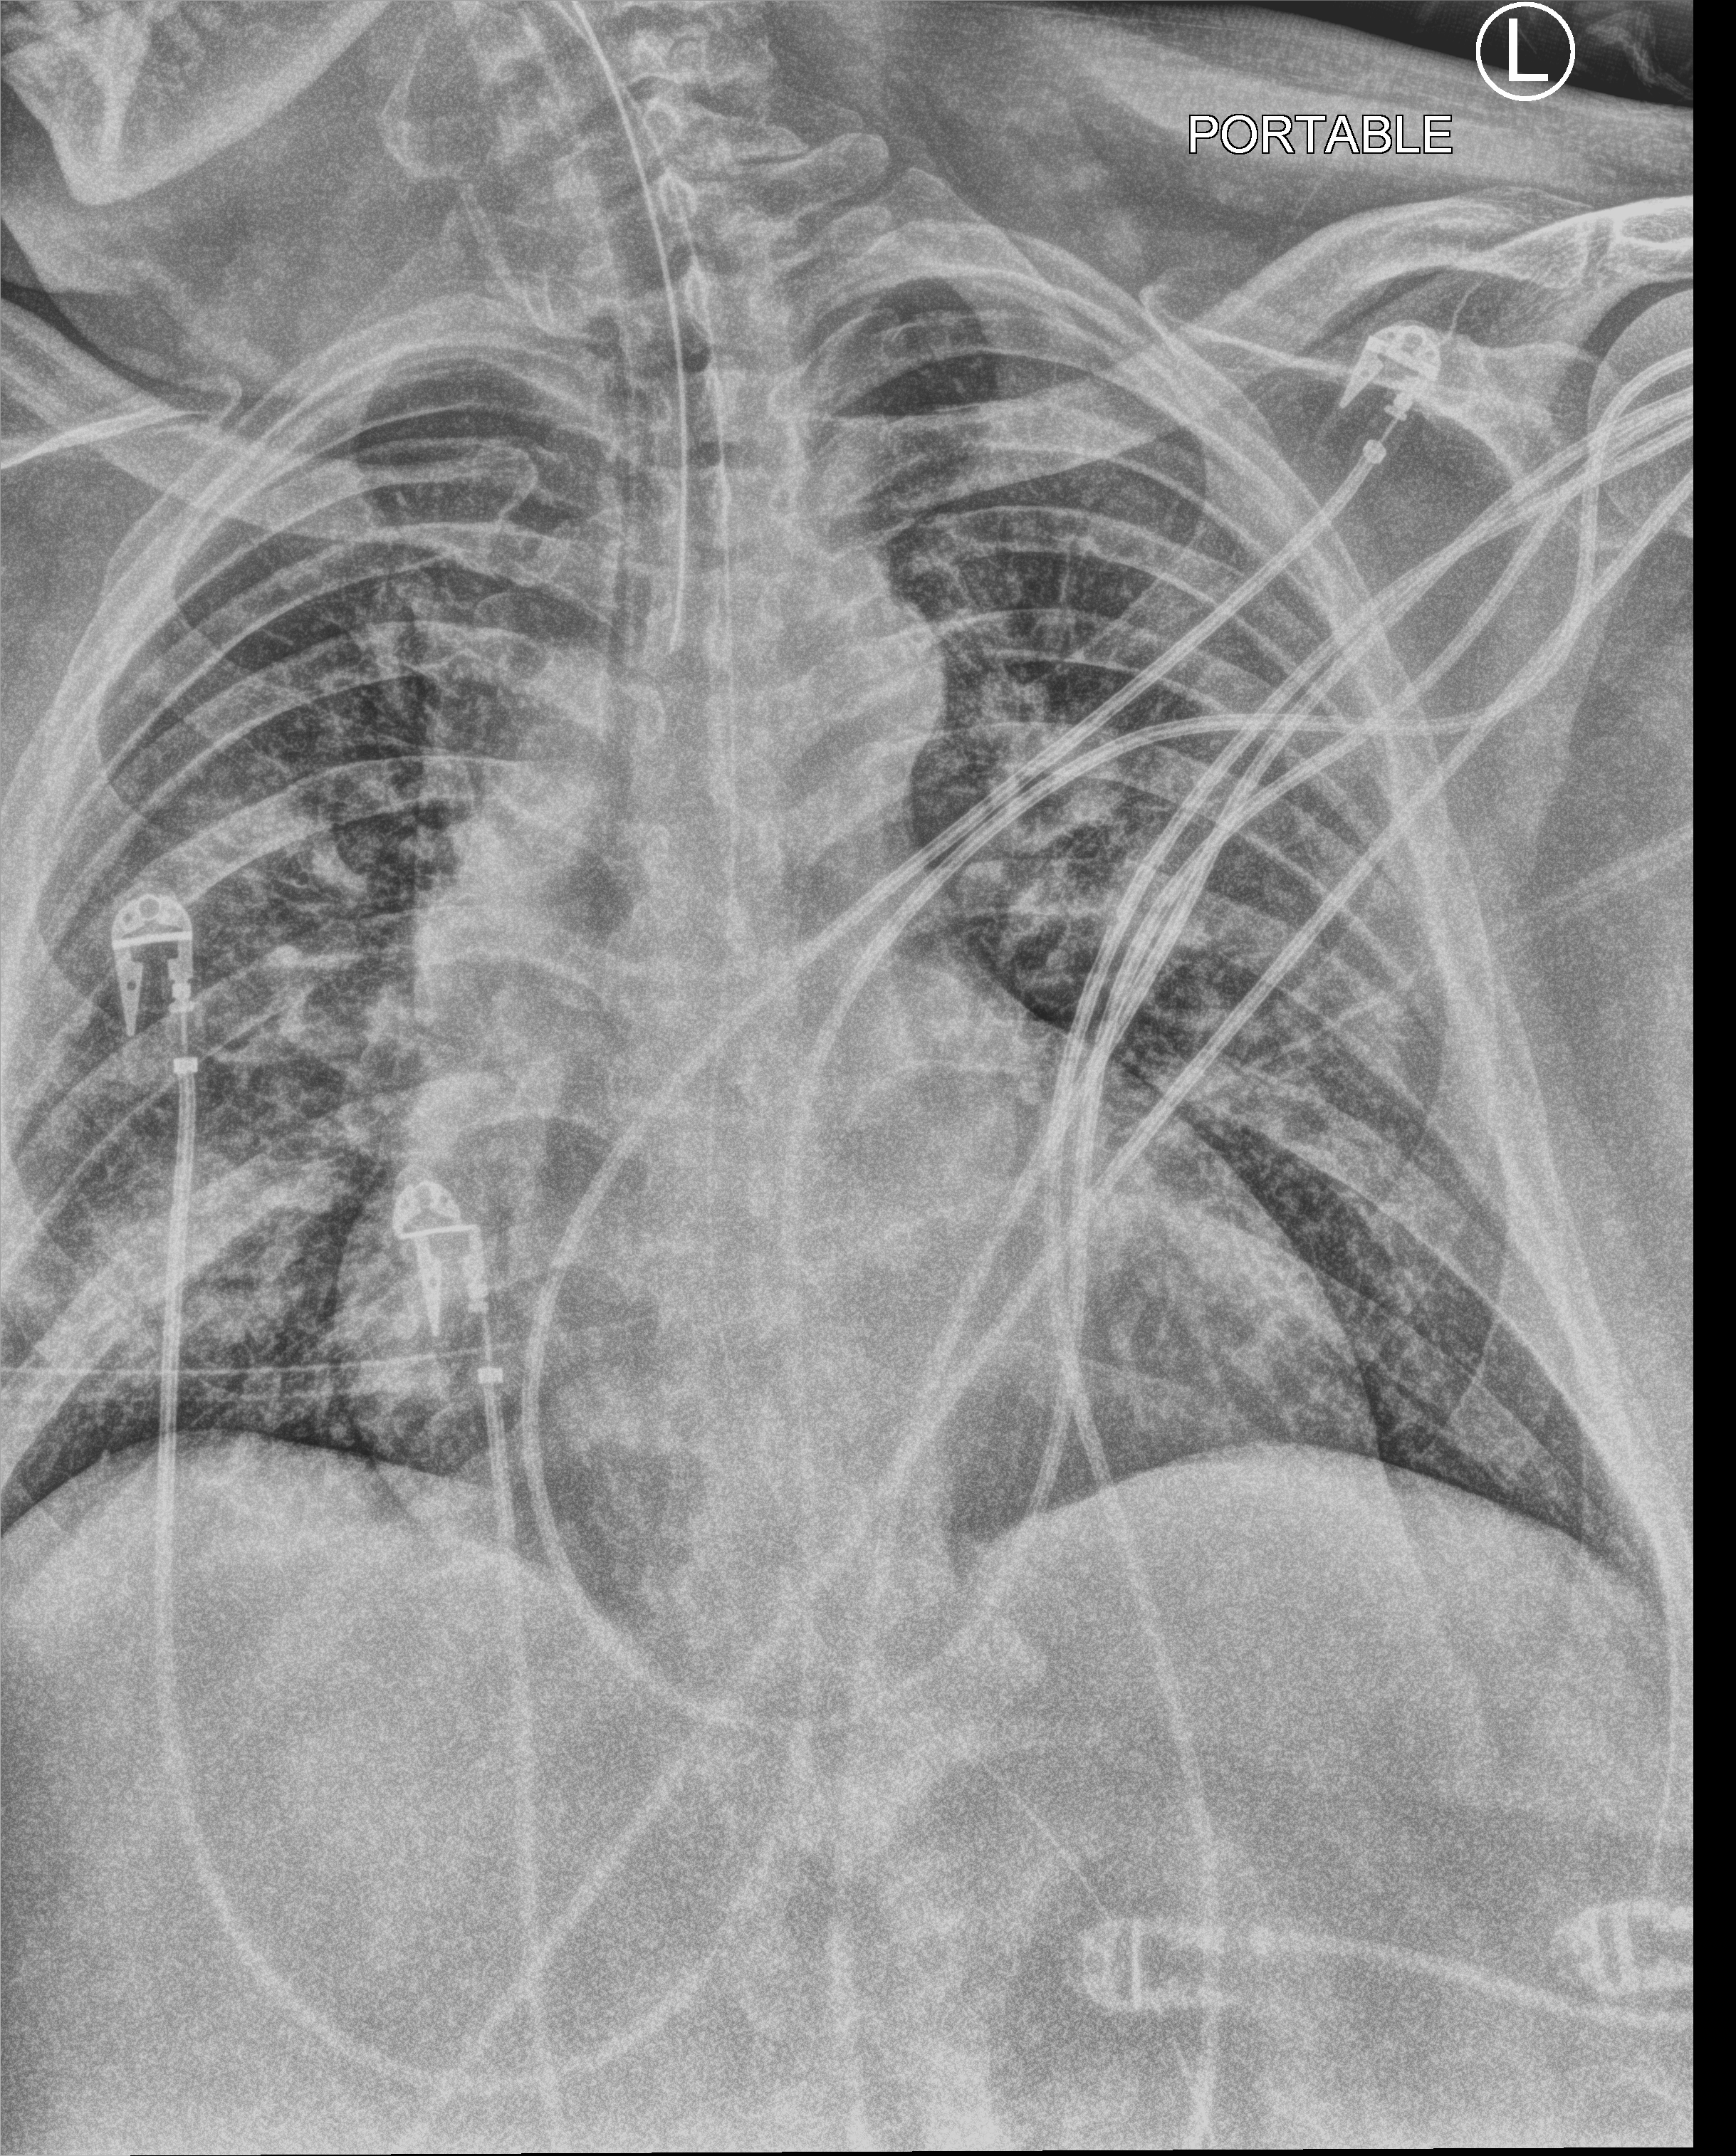
Chest X-ray (portable); anteroposterior (AP) projection. Patient hospitalised with COVID-19; male, aged 60–74 years.
From the hospital-stay record, not from the radiograph (when in the stay this image was taken is not recorded): length of hospital stay: 17 days.